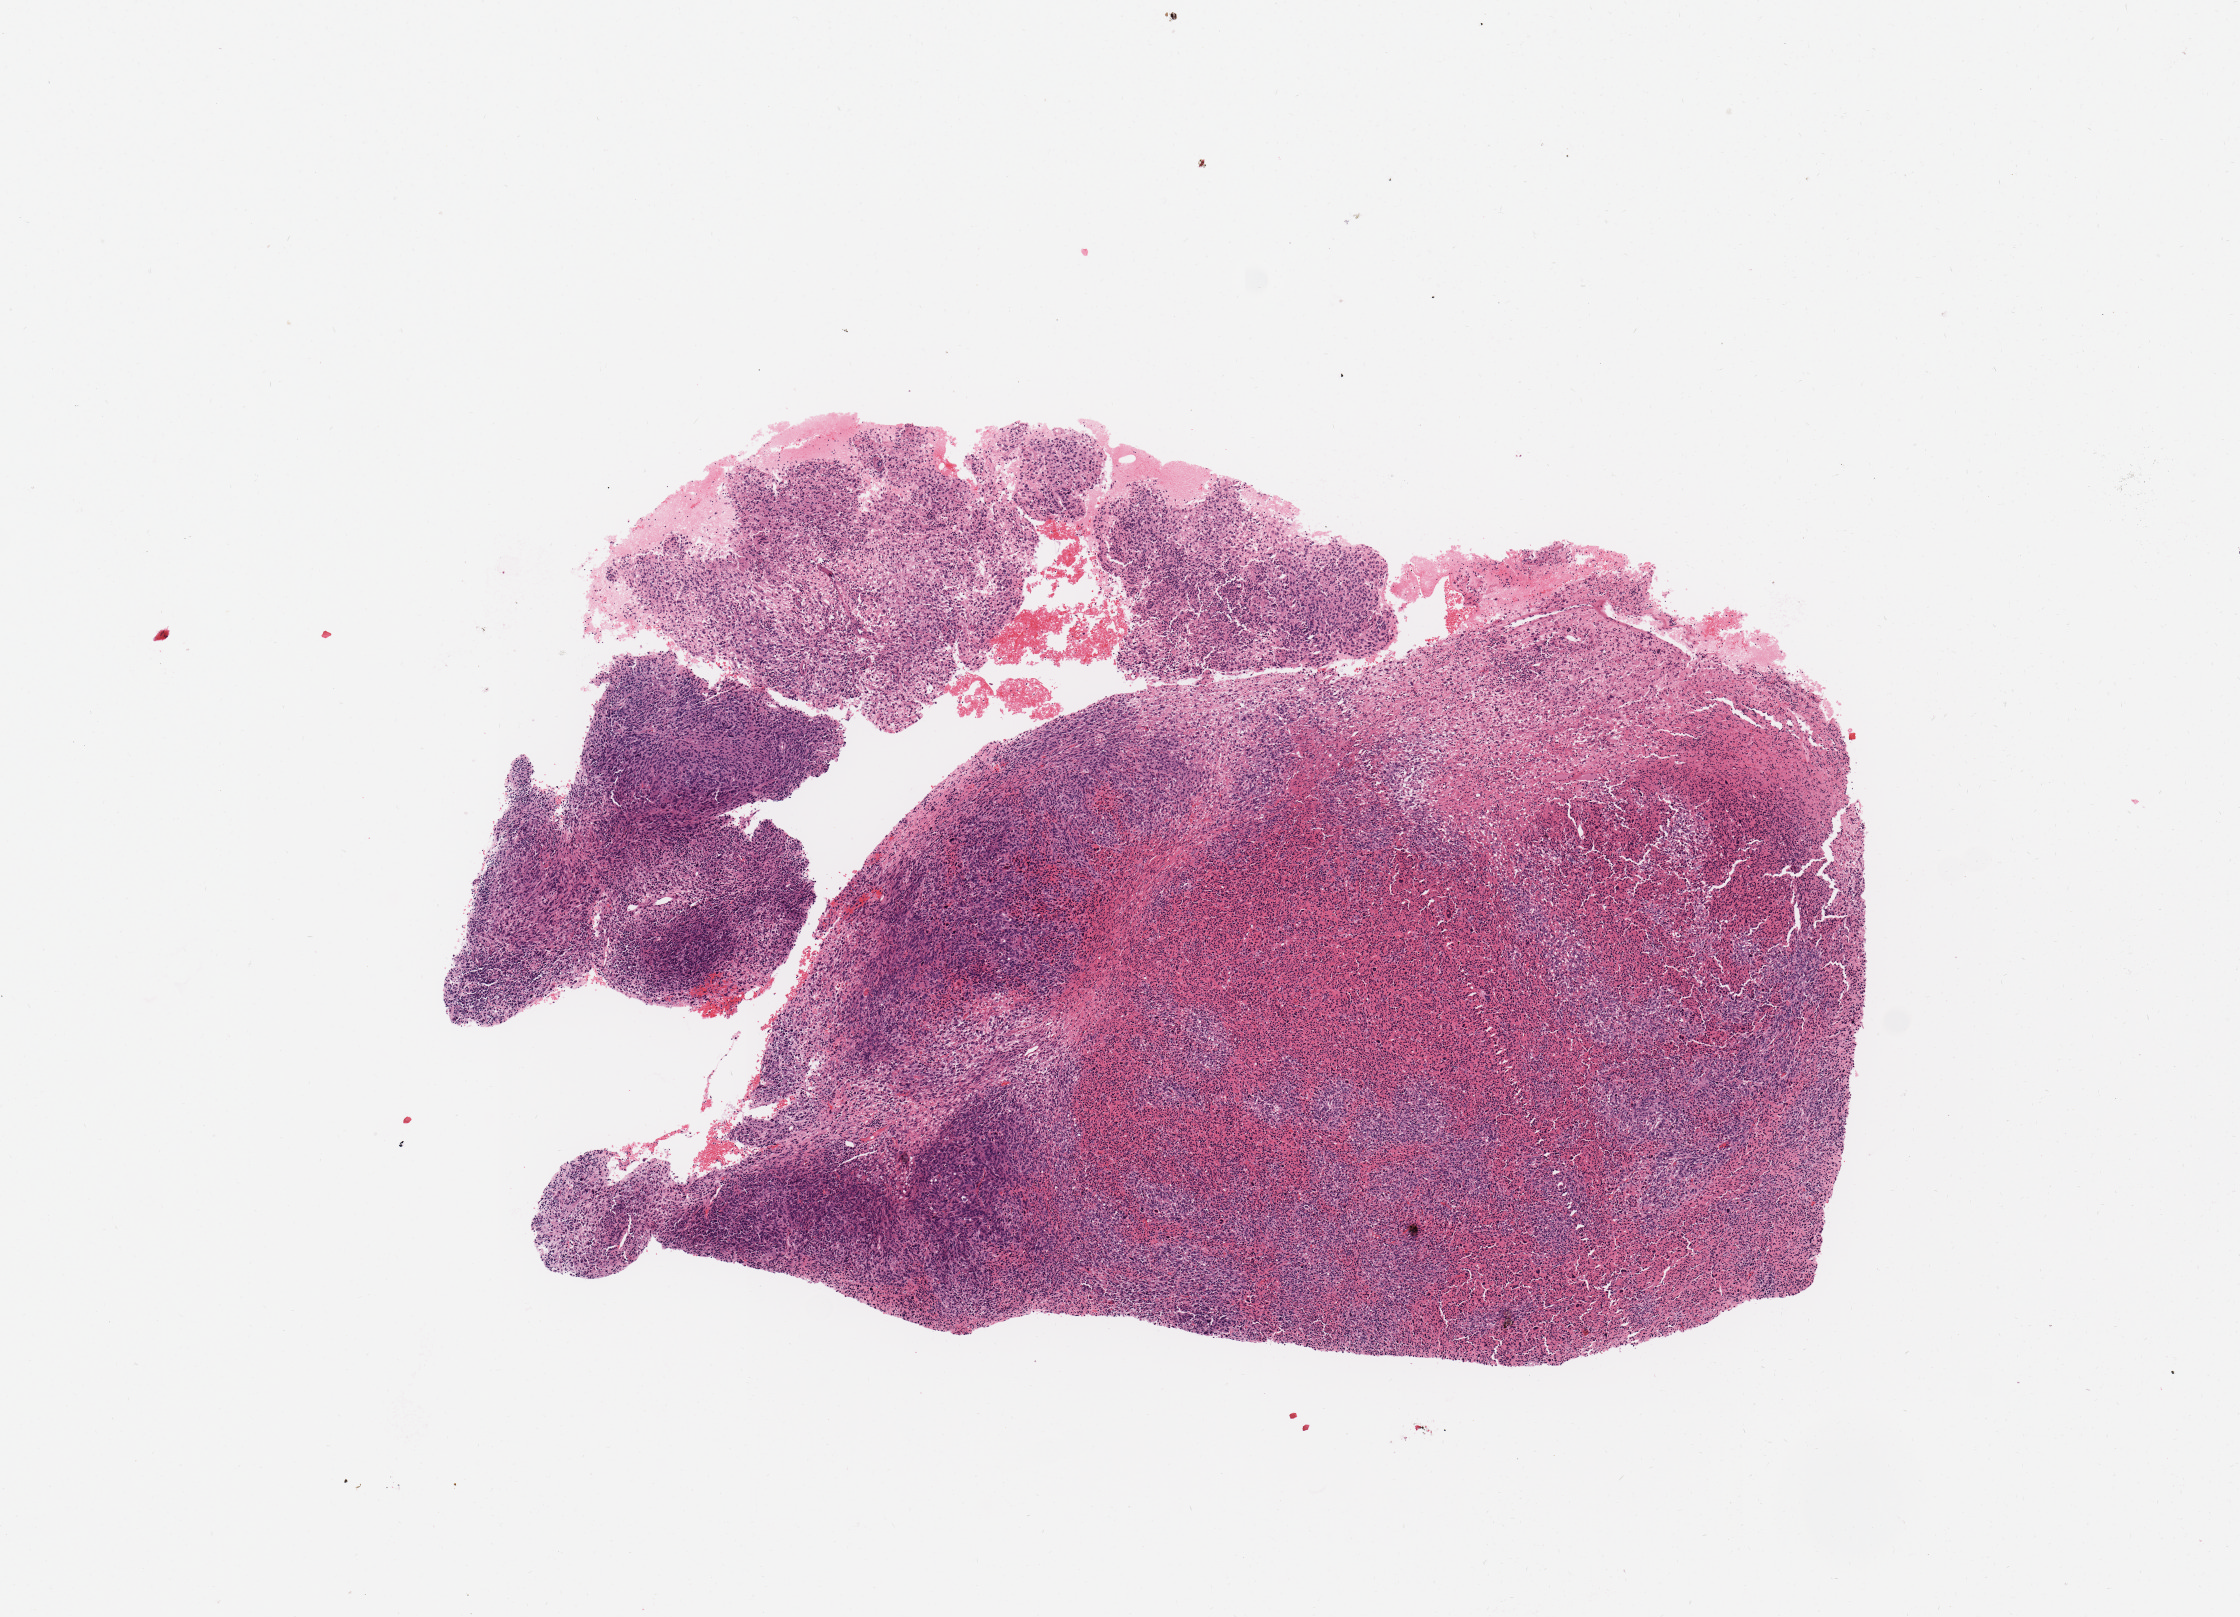
Hematoxylin and eosin (H&E) stained whole-slide image — low-resolution overview of the scanned area, about 8.9 x 6.4 mm (acquisition: 20x scan). Tumour tissue sample. Male, 56 y/o.
Primary tumour site (as recorded): retroperitoneum. Patient diagnosis (cohort enrolment): sarcoma (site not recorded at cohort level).